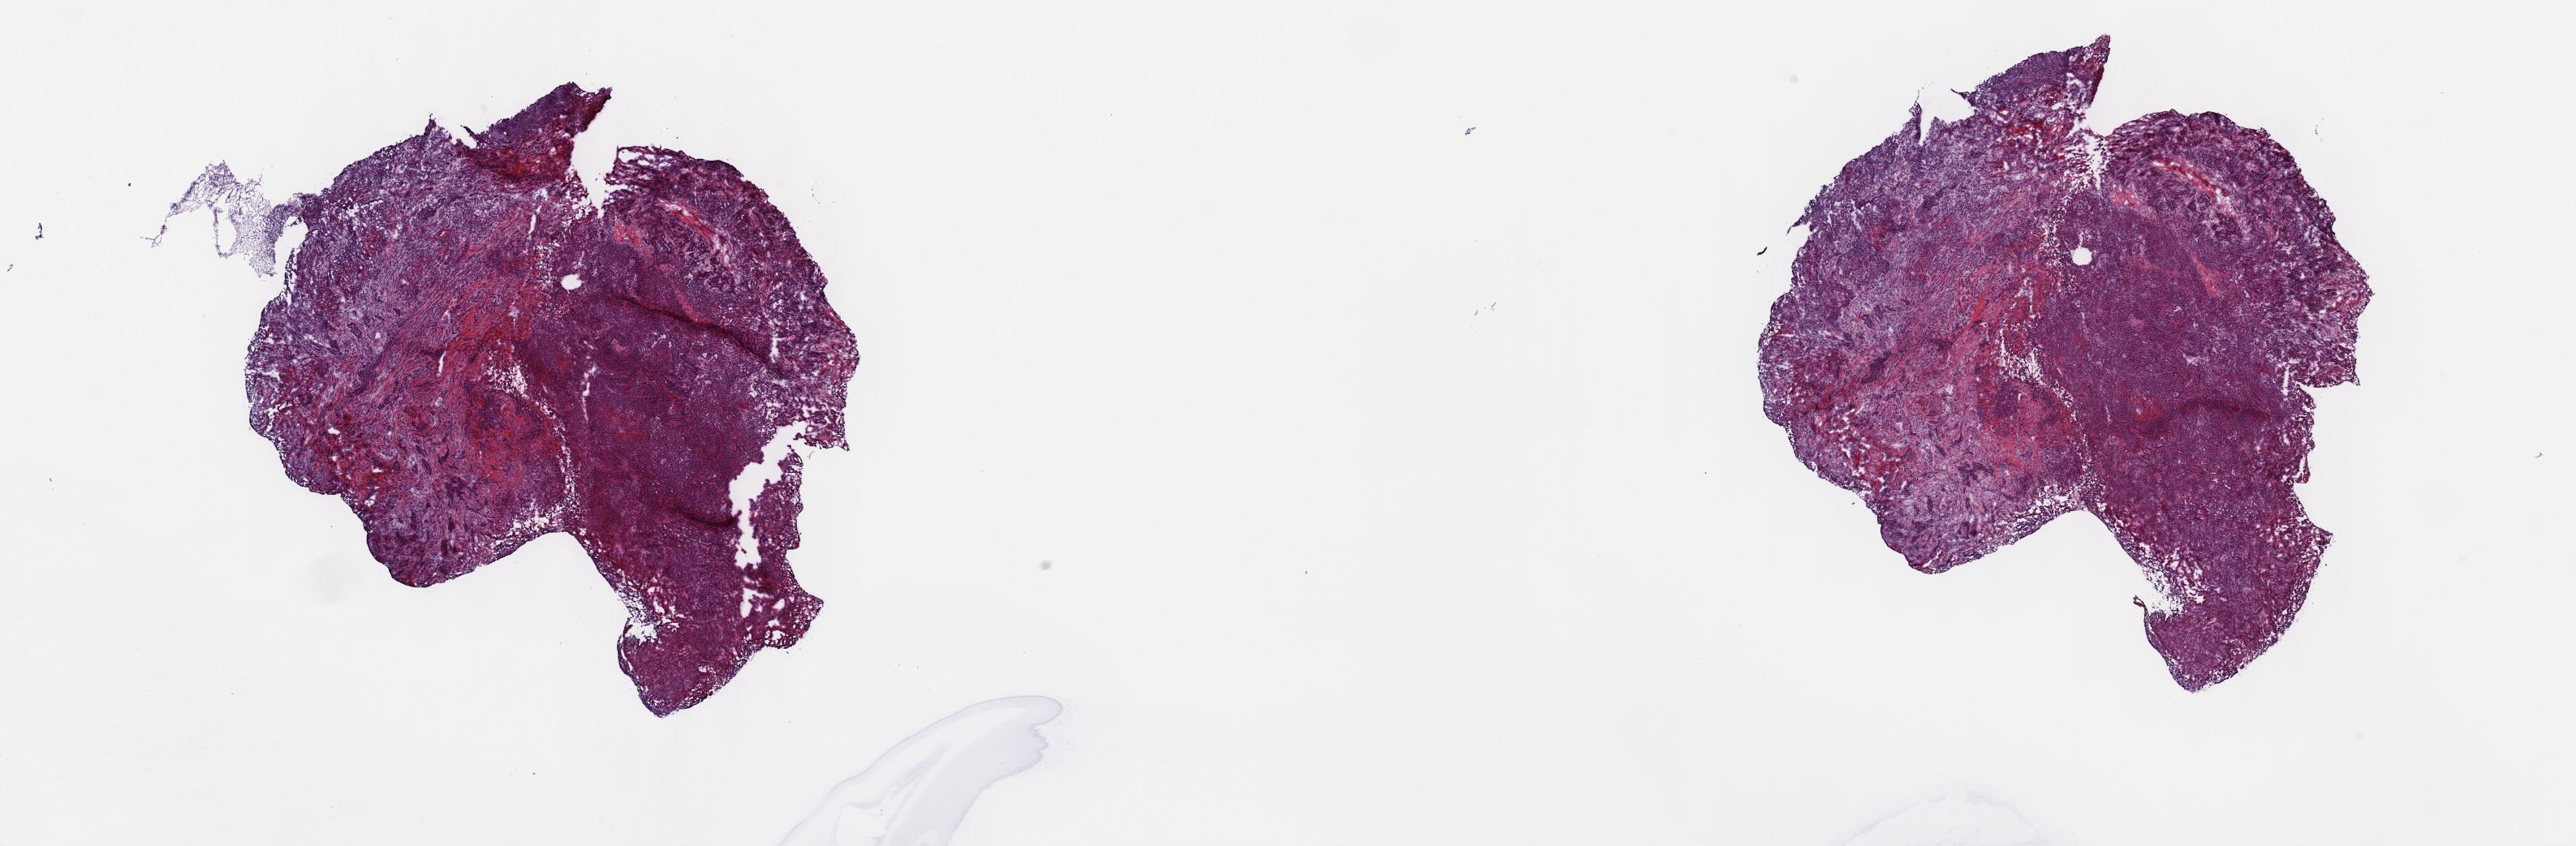
Digitized H&E-stained tissue section (whole slide), shown as a low-resolution overview of the whole scanned area (about 25.7 x 8.4 mm). Frozen section from the top of the tissue portion. Primary tumour sample from the mesothelium. Female patient; age at initial diagnosis 53 years. Composition of this section per pathologist review: tumour cells 100%, tumour nuclei 65%, normal cells 0%, stromal cells 0%, necrosis 0%. Inflammatory infiltration, as recorded: lymphocyte infiltration 2%, monocyte infiltration 0%, neutrophil infiltration 0%.
* laterality: left
* TNM: T3 N2 M0
* pathologic diagnosis: Epithelioid mesothelioma, malignant (pleura, NOS)
* AJCC pathologic stage: III